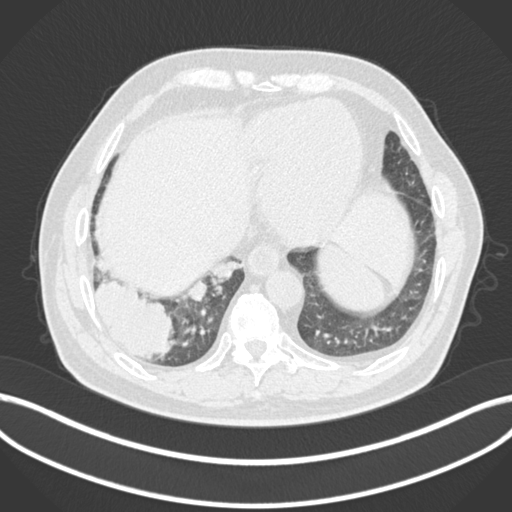
Chest CT, one axial slice. Slice 29 of 200 in the series (ordered by position). Reconstruction kernel B30f. Lung window (W 1500 / L -600 HU). 512 × 512 image matrix, field of view 400 × 400 mm. Male patient, age 59 years.
Outlined on this slice (rectangle marked by the reading radiologist):
- lung tumour (recorded histology: adenocarcinoma): box from (x=92, y=277) to (x=179, y=362) px